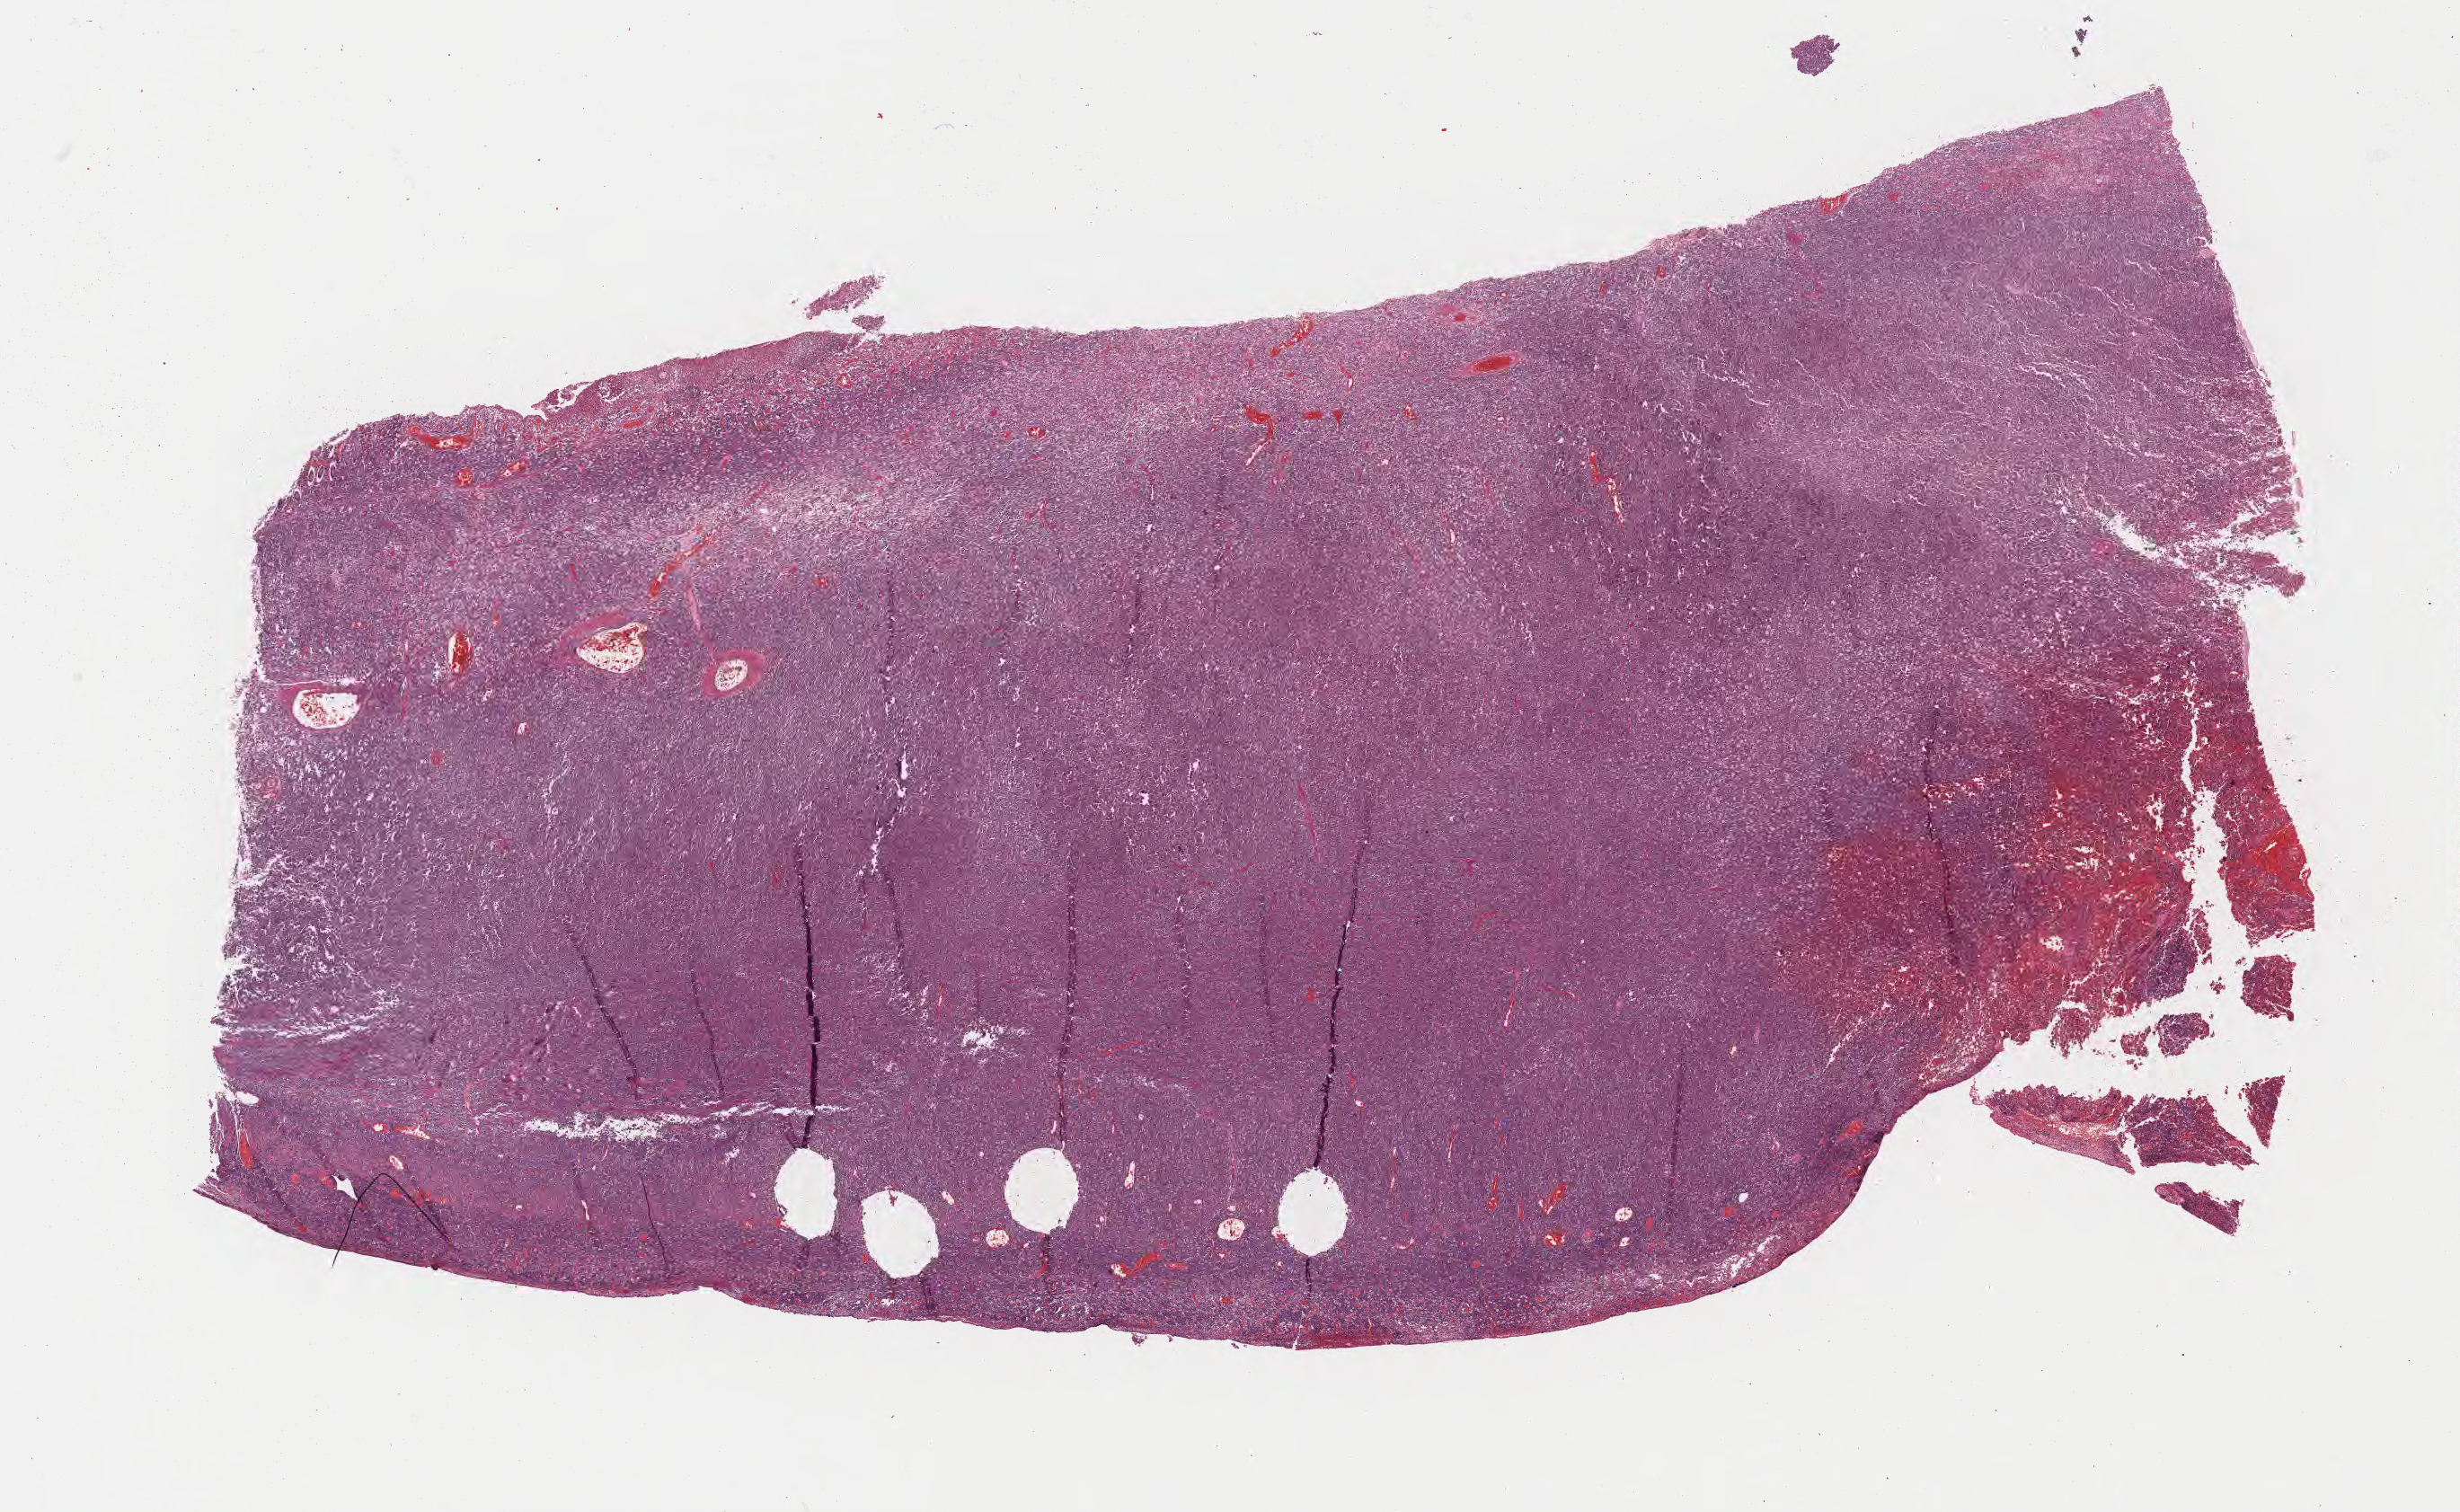
Digitized haematoxylin and eosin-stained section — shown as a low-resolution overview of the whole scanned area (about 22.1 x 13.6 mm), formalin-fixed paraffin-embedded section, specimen: primary tumor. Patient: female, age at initial diagnosis 6 years. Composition of this section per pathologist review: tumor cells 95%, tumor nuclei 95%, stromal cells 5%, necrosis 0%, normal cells 0%. Infiltration values recorded for this section: lymphocyte infiltration 50%, monocyte infiltration 20%, neutrophil infiltration 5%.
Histologic diagnosis: Burkitt lymphoma, NOS. Ann Arbor stage (patient): Stage IV.